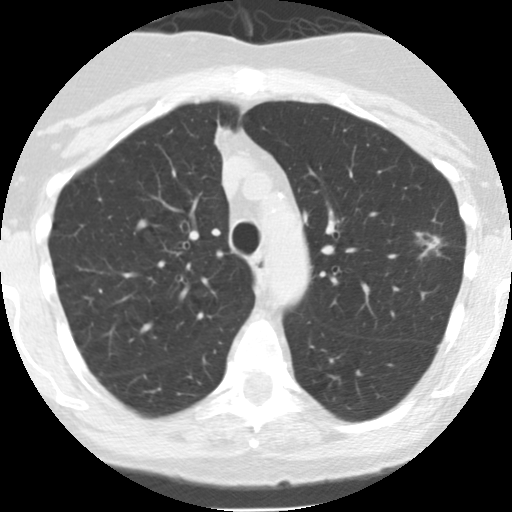
Low-dose screening chest CT, one axial slice; position 106 of 145 along the scan axis; lung window (W 1500 / L -600 HU); 512 × 512 image matrix.
Annotated regions visible in this slice (outlined manually by an expert reader):
- lesion 1 (tumor, upper lobe of left lung): bounding box [x1, y1, x2, y2] px = [416, 232, 441, 258]